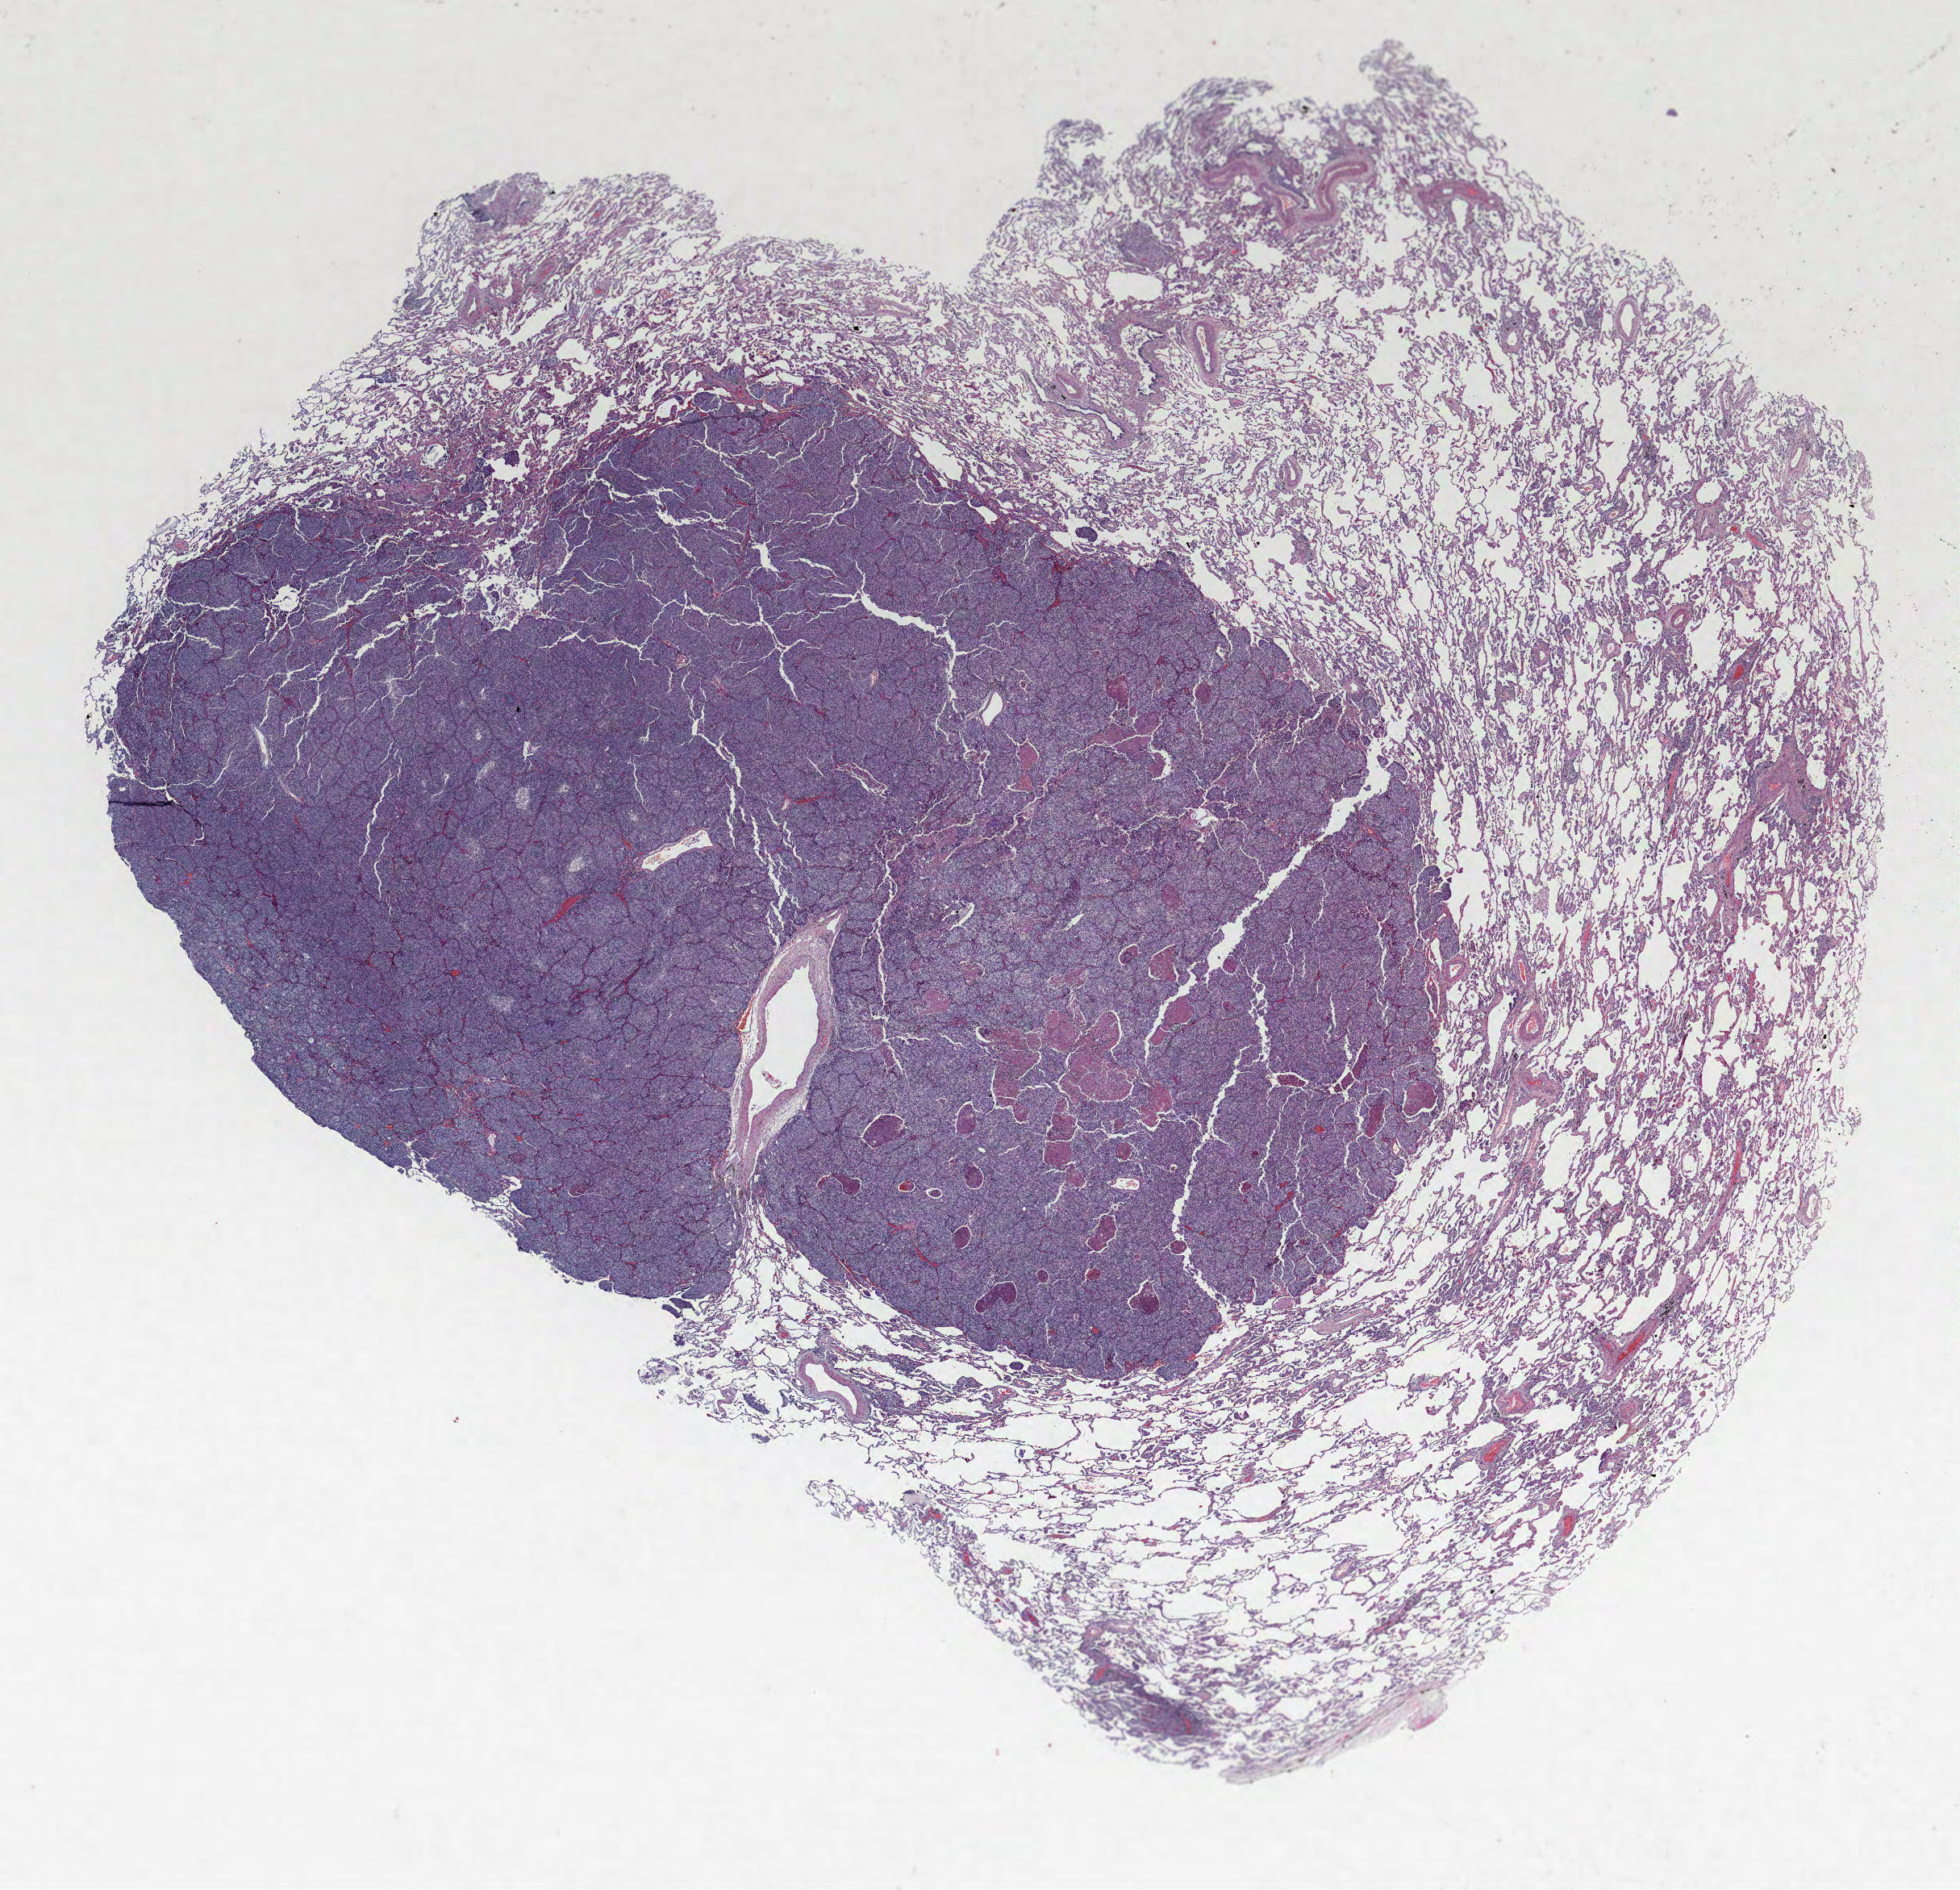
Whole-slide histology image, H&E, low-resolution overview of the scanned area, about 19.4 x 18.7 mm (slide scanned at 40x); formalin-fixed paraffin-embedded (FFPE) section; lung tissue. Male patient, aged 65 at enrolment. Former smoker at enrolment. Grade: poorly differentiated (G3).
* tumour size (pathology): 17 mm
* ICD-O-3 topography: upper lobe of lung (C34.1)
* participant's lung-cancer diagnosis: Adenocarcinoma, NOS
* primary tumour location (clinical record): right upper lobe
* stage (AJCC 6th edition): IA